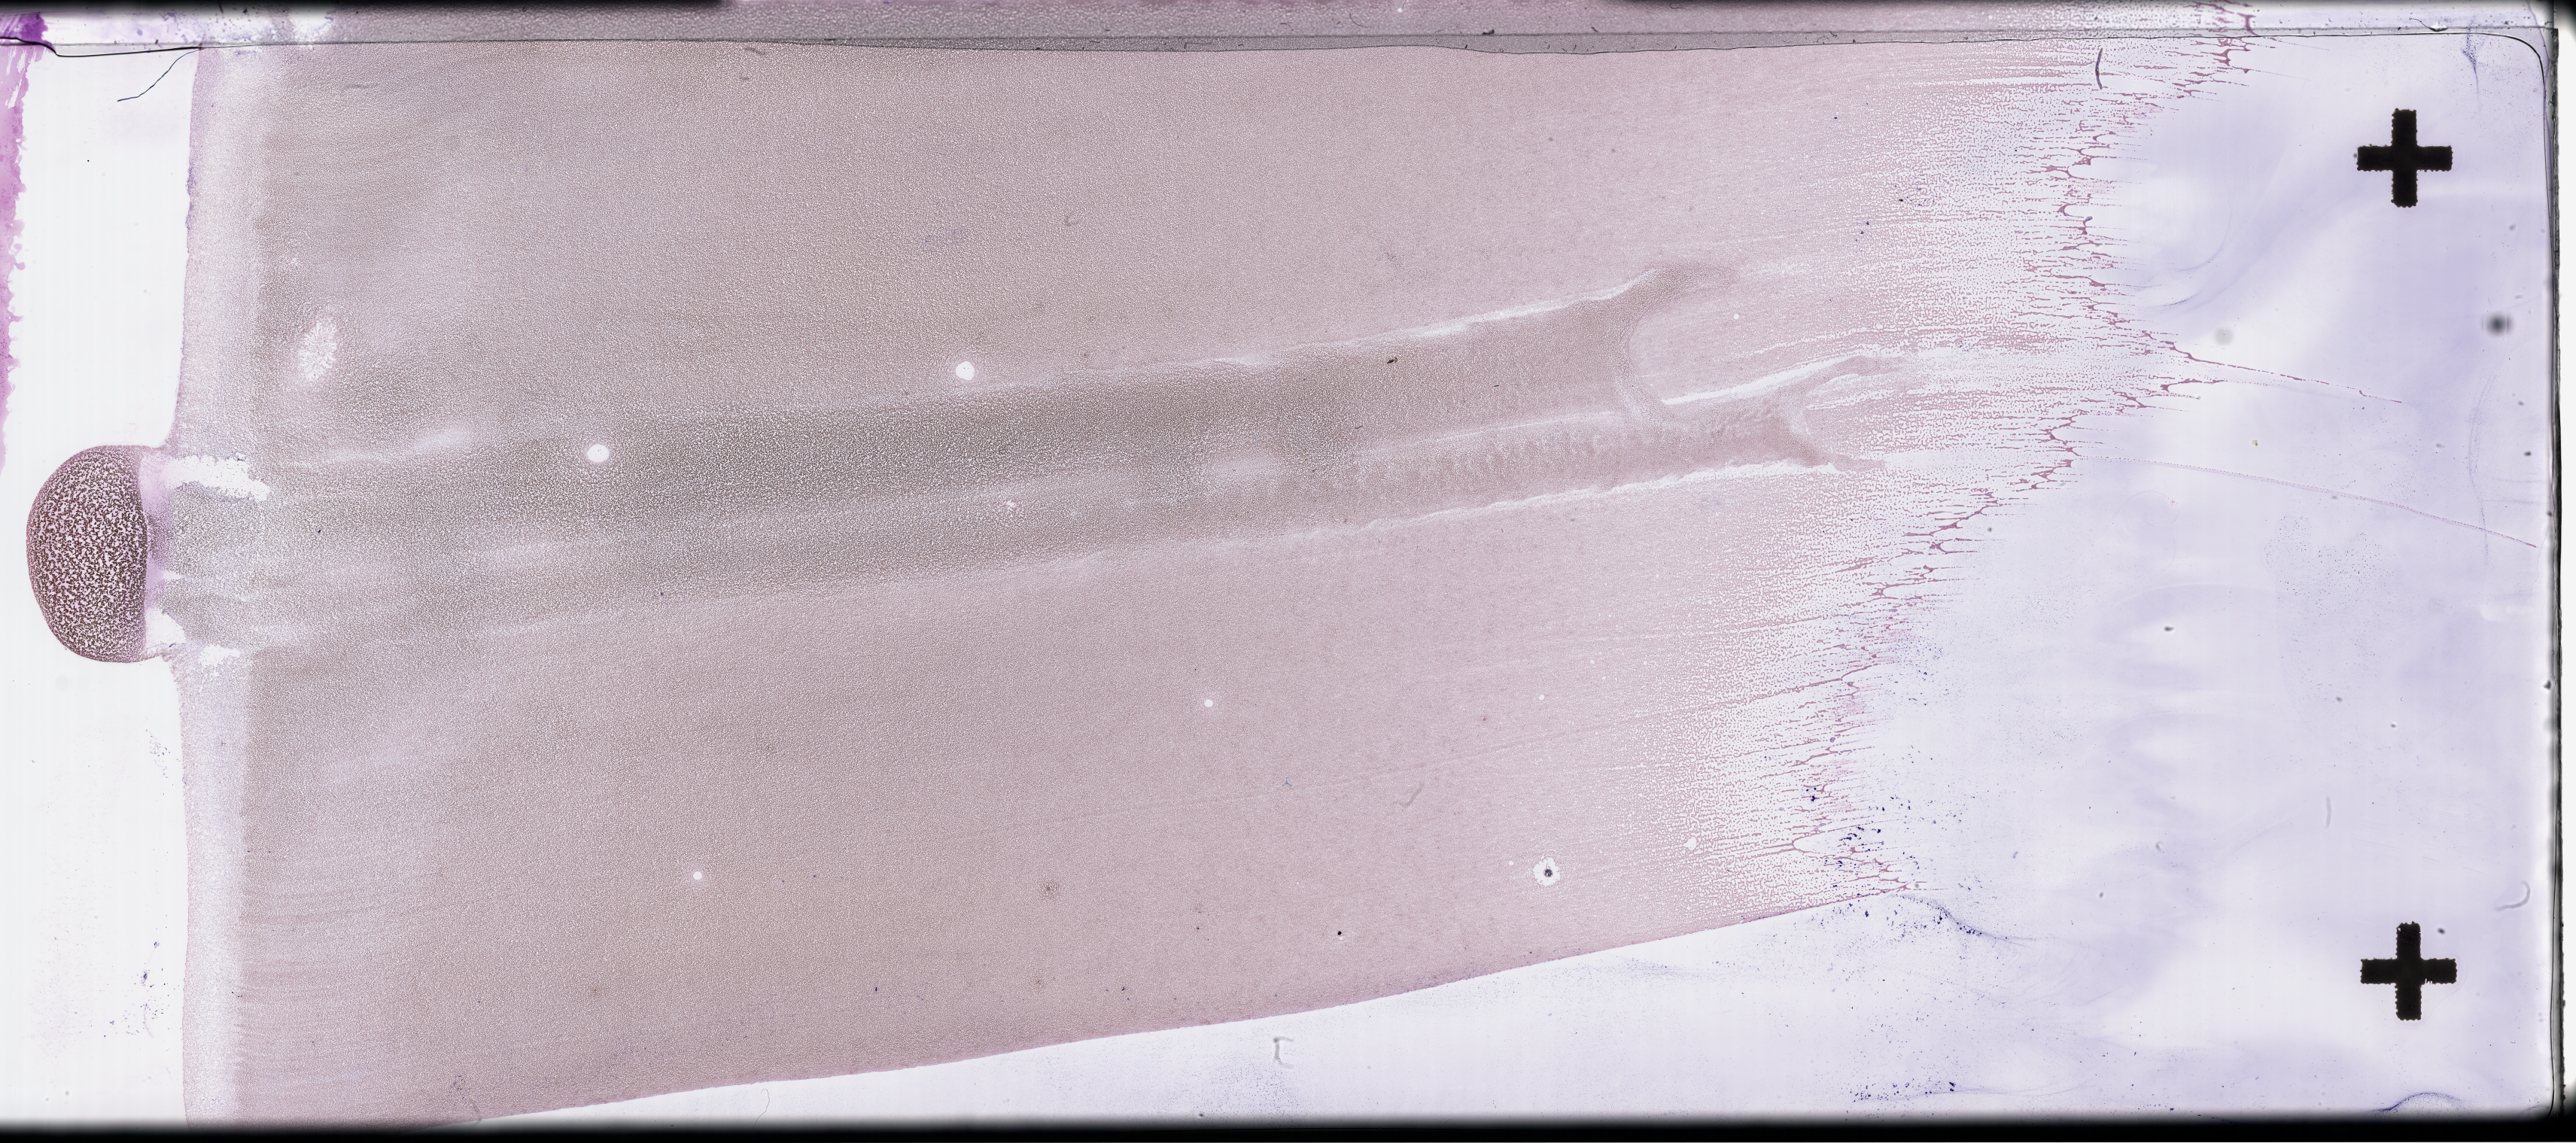
Whole-slide image of a whole blood smear, Wright-Giemsa stain — whole scanned area (about 55.3 x 24.5 mm) shown as a low-resolution overview, collected at baseline (before treatment). Patient: male.
Patient diagnosis: Plasma Cell Myeloma.